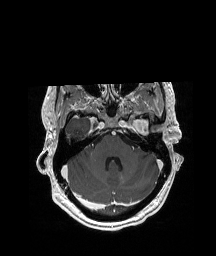
Brain MRI from a brain-tumour surgery series, one axial slice; T1-weighted post-contrast; 1 mm slice thickness; 216 × 256 image matrix, field of view 228 × 270 mm. From the clinical record (not read from this slice): histopathology: Glioblastoma; WHO grade: 4; IDH mutation: no; tumour location: Left Anterior/Superior Temporal.
Outlined on this slice (expert manual segmentation):
- tumour: bounding box <139,113,154,130> (left, top, right, bottom; pixels)